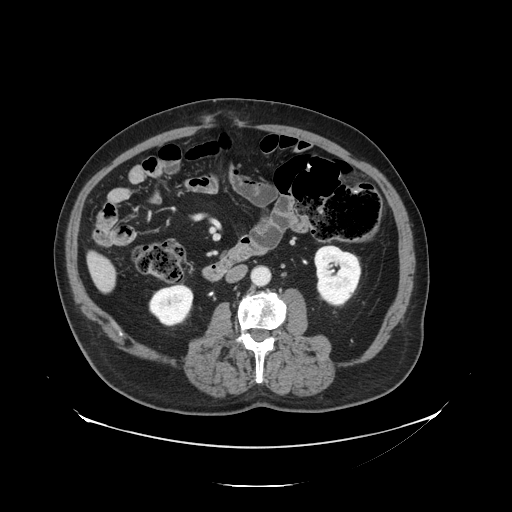
Contrast-enhanced abdominal CT, one axial slice. Position 35 of 138 along the scan axis. Reconstruction kernel STANDARD. 120 kVp. Soft-tissue window (W 400 / L 40 HU). 2.5 mm slice thickness. 512 × 512 image matrix, field of view 497 × 497 mm. Male patient, age 77 years. Case-level facts recorded for this patient, not image findings: diagnosis: colorectal cancer liver metastases, imaged before liver resection; multiple liver metastases: no; largest metastasis: 1.5 cm; disease in both lobes: no.
Annotated regions visible in this slice (outlined manually by an expert reader):
- liver: bounding box (x1, y1, x2, y2) in pixels: (90, 255, 116, 291)
- planned liver remnant (the part of the liver to remain after resection): (90, 254, 111, 275)